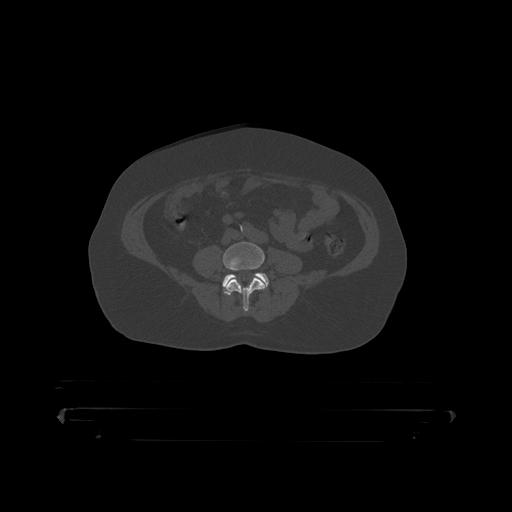
CT including the spine, one axial slice. Reconstruction kernel STANDARD. Bone window (W 1800 / L 400 HU). 512 × 512 image matrix, field of view 650 × 650 mm. Male patient, age 60 years. Case-level facts recorded for this patient, not image findings: primary cancer: prostate.
Structures marked on this image (semi-automatic segmentation, software-assisted and operator-edited):
- L4 vertebra: bounding box [x1, y1, x2, y2] px = [223, 242, 265, 312]
- L5 vertebra: [223, 273, 269, 294]